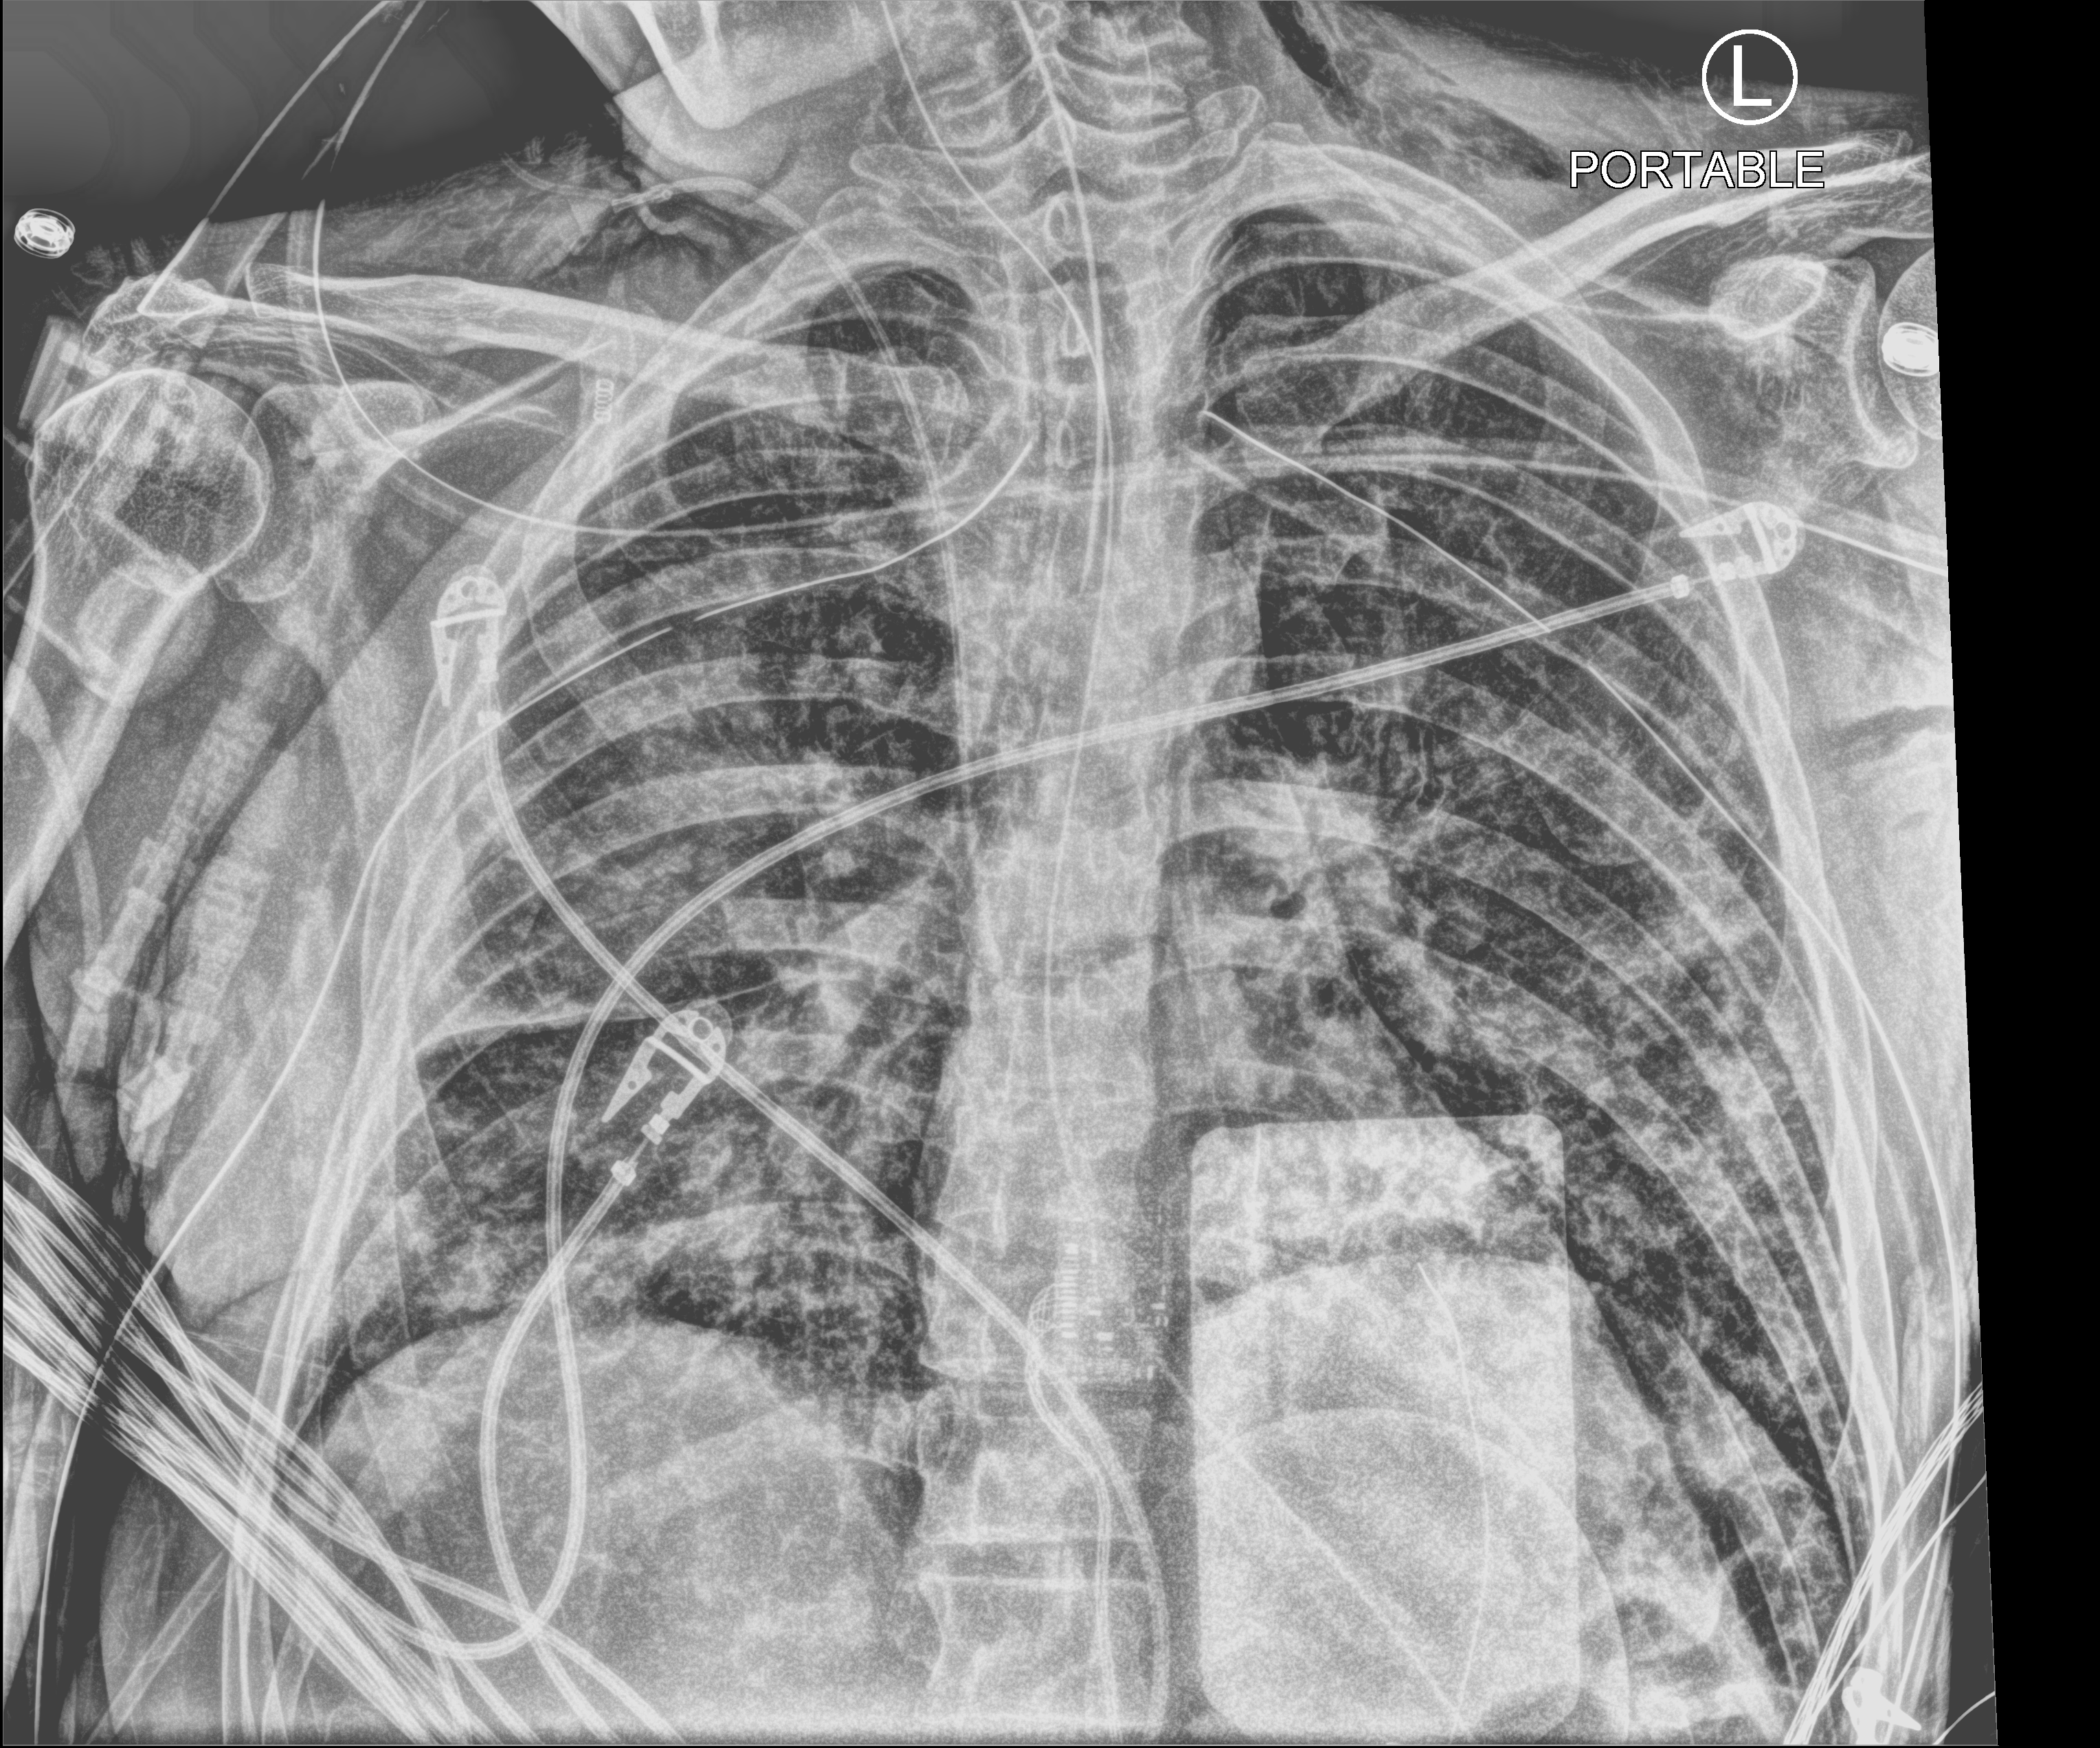
Bedside chest radiograph (computed radiography); anteroposterior (AP) projection. Male patient hospitalised with COVID-19, age 18–59 years.
Admission-level facts for this patient (not findings on this image; timing relative to this image not recorded):
- hypertension (admission record): yes
- mechanically ventilated during this hospital stay: yes
- chronic kidney disease (admission record): no